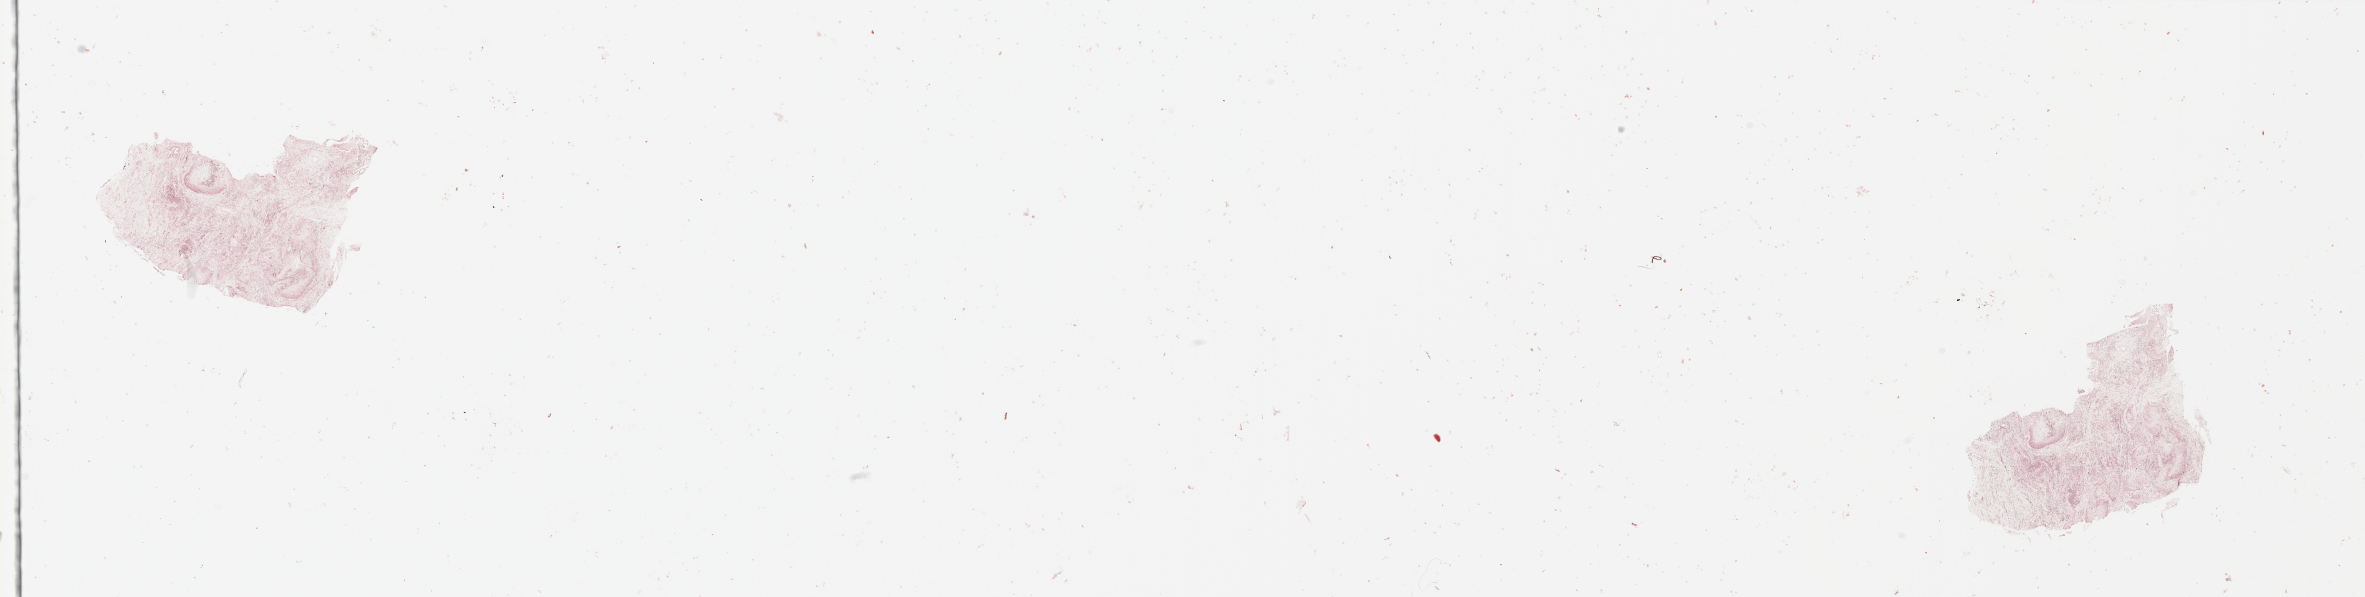
Hematoxylin and eosin (H&E) stained whole-slide image — whole scanned area (about 37.4 x 9.4 mm) shown as a low-resolution overview; head and neck, tissue type not recorded. Male, 64 y/o.
Patient diagnosis: Squamous cell carcinoma, NOS.